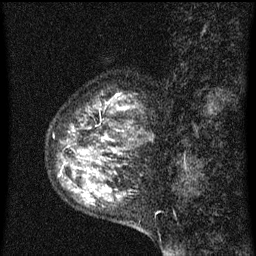
Breast MRI (dynamic contrast-enhanced), one sagittal slice. Position 23 of 60 along the scan axis. Dynamic contrast-enhanced series, image 2 of 3 at this slice position (ordered by acquisition). 1.5 T. TE 4.2 ms, TR 8 ms. 2 mm slice thickness. 256 × 256 image matrix. Female patient, age 55 years.
Structures marked on this image (semi-automatically segmented with operator editing):
- analysis volume of interest (the breast-tissue region the enhancement analysis was run in; not a lesion): bounding box <50,96,157,151> (left, top, right, bottom; pixels)
- tumour enhancement mask (voxels above the 70 % enhancement threshold inside the analysis volume of interest): <72,106,129,141>